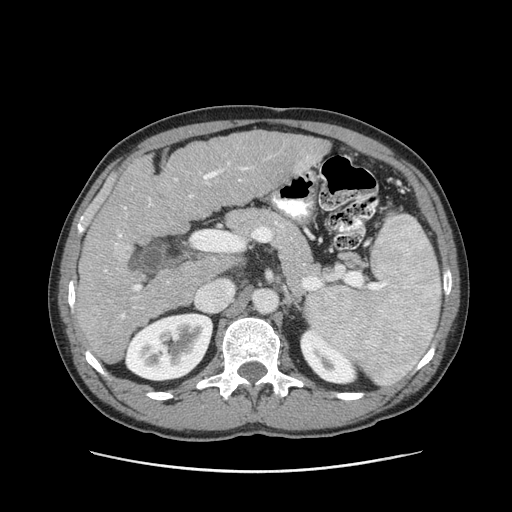
Contrast-enhanced abdominal CT (liver protocol), one axial slice; slice 51 of 93 in the series (ordered by position); reconstruction kernel STANDARD; 120 kVp; soft-tissue window (W 400 / L 40 HU); 2.5 mm slice thickness; 512 × 512 image matrix. From the clinical record (not read from this slice): diagnosis: hepatocellular carcinoma (patient treated with transarterial chemoembolisation; whether this scan precedes or follows treatment is not stated here); TNM stage (as recorded): Stage-II; Child-Pugh class: A; tumour nodularity: multinodular; tumour size: 1 cm.
Annotated regions visible in this slice (semi-automatic segmentation, software-assisted and operator-edited):
- liver parenchyma outside the tumour (the mass and vessels are separate outlines, so this box may not span the whole liver): bounding box (x1, y1, x2, y2) in pixels: (74, 130, 328, 364)
- liver vessels: (104, 156, 309, 318)